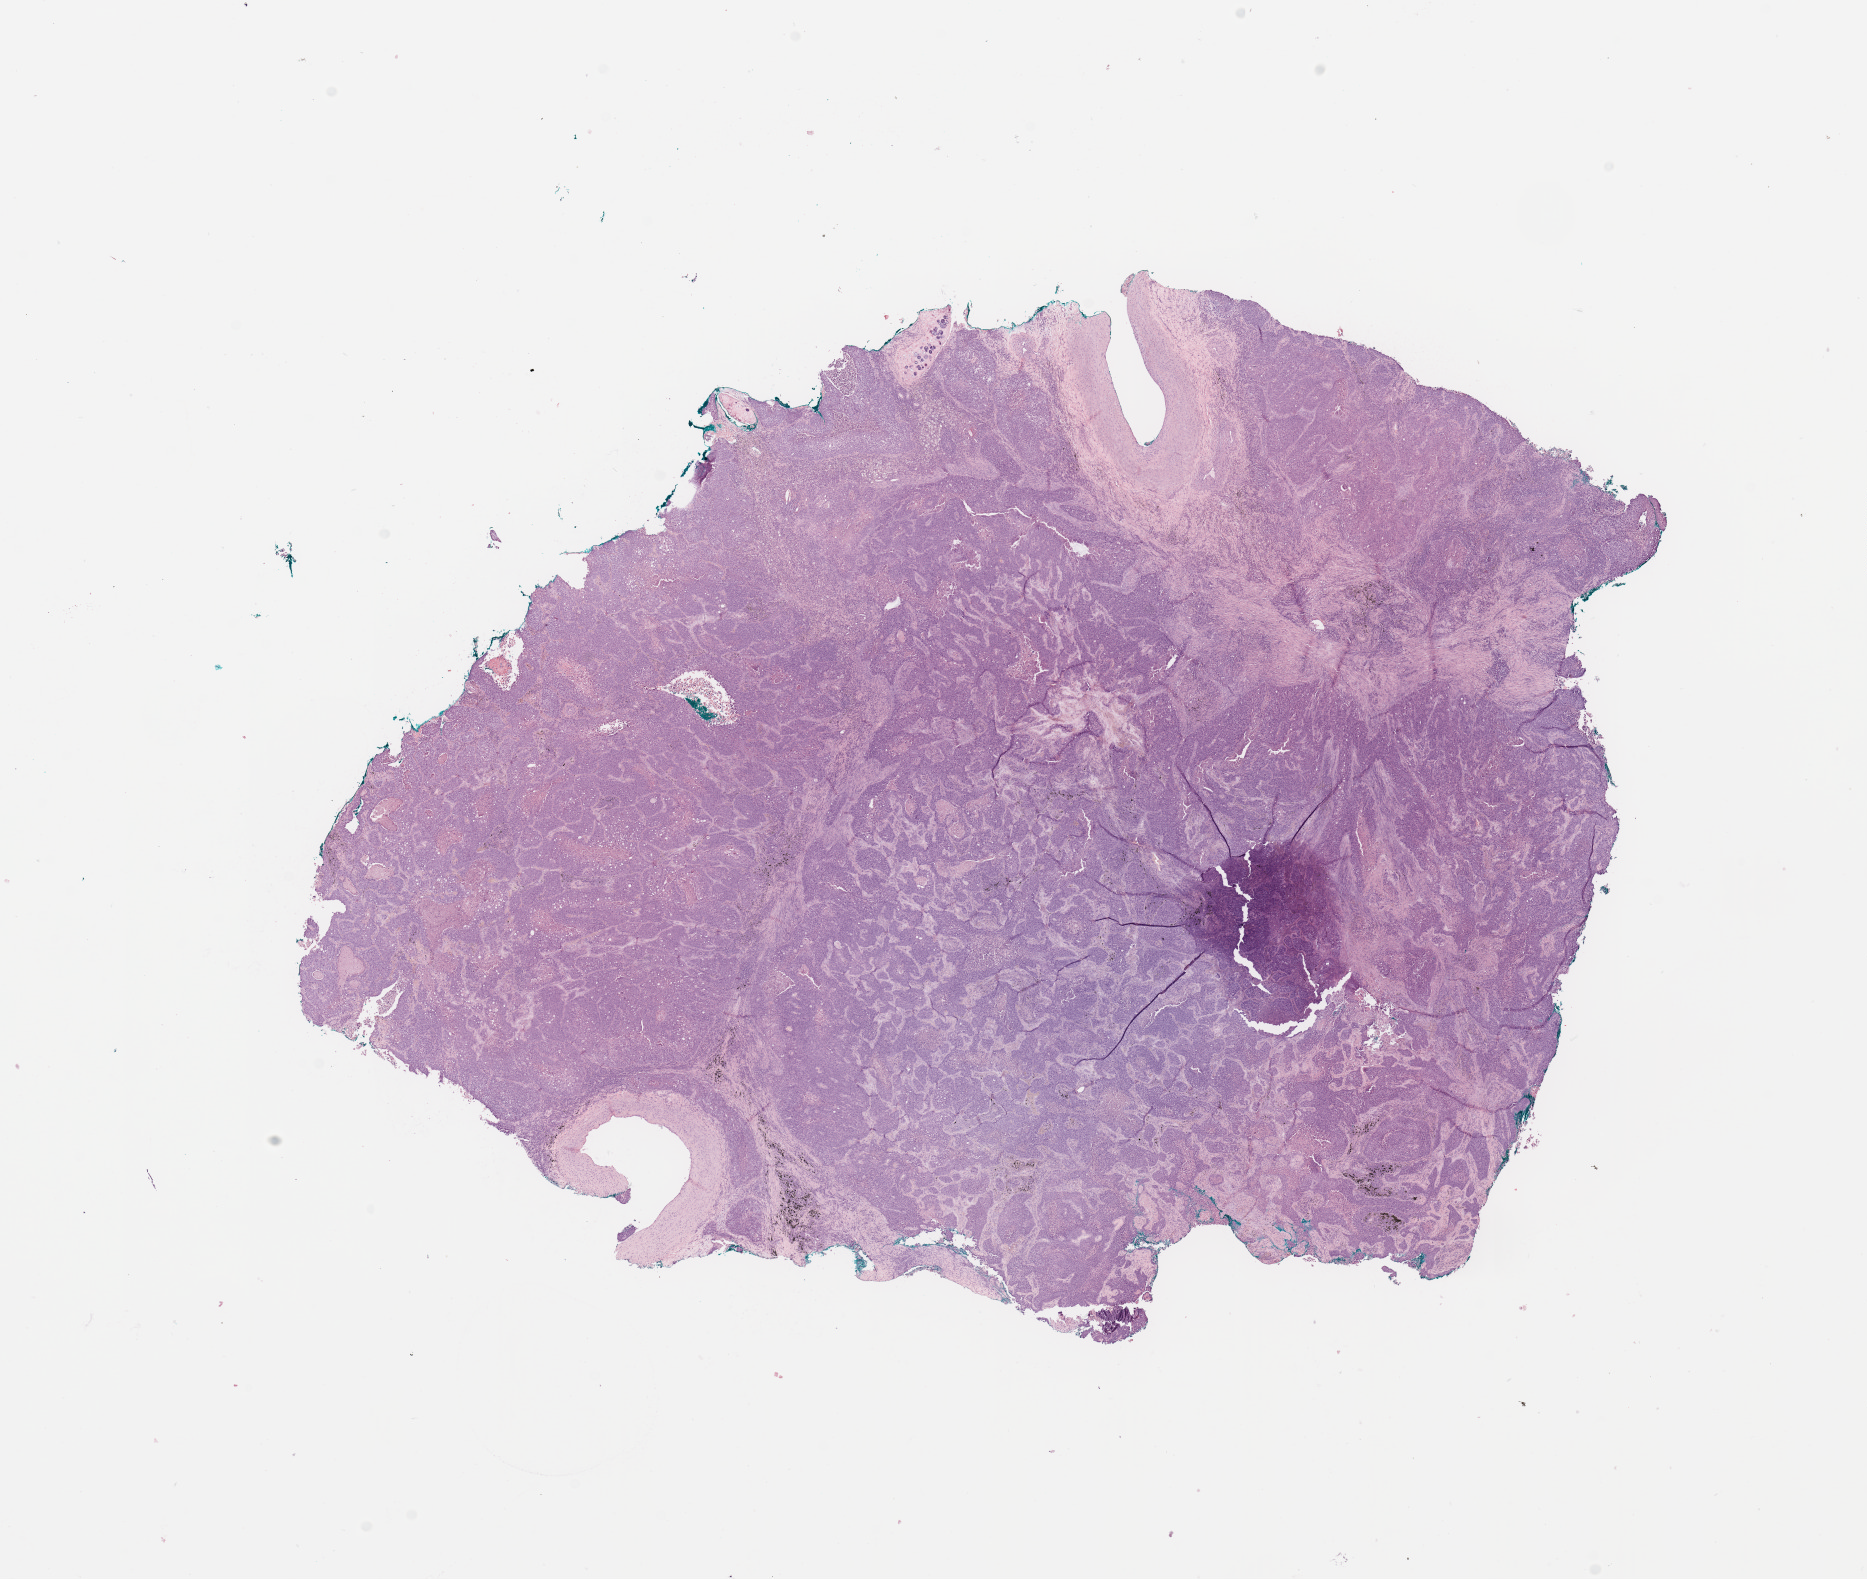
Whole-slide histology image, H&E, low-resolution overview of the scanned area, about 14.8 x 12.5 mm. Tumour tissue sample, sampled site: lung. Patient: male, age 75 years. Histologic grade: G2 (moderately differentiated). Slide review estimates, as recorded: tumour nuclei 80%, necrosis 8%.
- diagnosis: Squamous cell carcinoma, NOS
- primary tumour site (as recorded): right lower lobe
- AJCC pathologic stage: IIIA